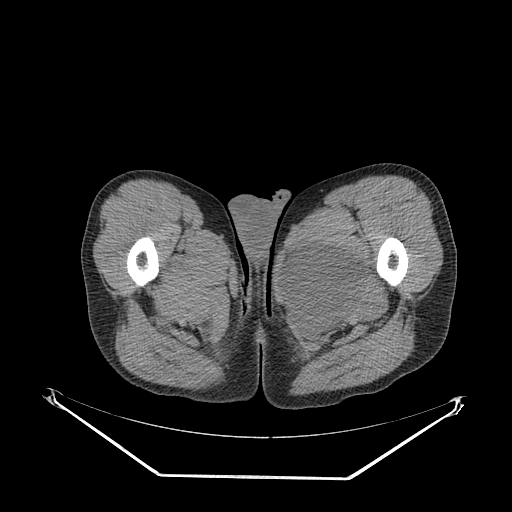
CT of an extremity soft-tissue mass (from a PET/CT study), one axial slice. Slice 38 of 267 in the series (ordered by position). Soft-tissue window (W 400 / L 40 HU). 3.75 mm slice thickness. 512 × 512 image matrix. Male patient. Case-level facts recorded for this patient, not image findings: histological type: pleiomorphic liposarcoma; grade: high; site of the primary tumour: left thigh.
Outlined on this slice (expert contour drawn on MRI and transferred to this co-registered scan by the dataset authors):
- gross tumour volume including surrounding oedema: box from (x=285, y=237) to (x=364, y=328) px
- gross tumour volume (mass): (x=285, y=242)–(x=362, y=316)